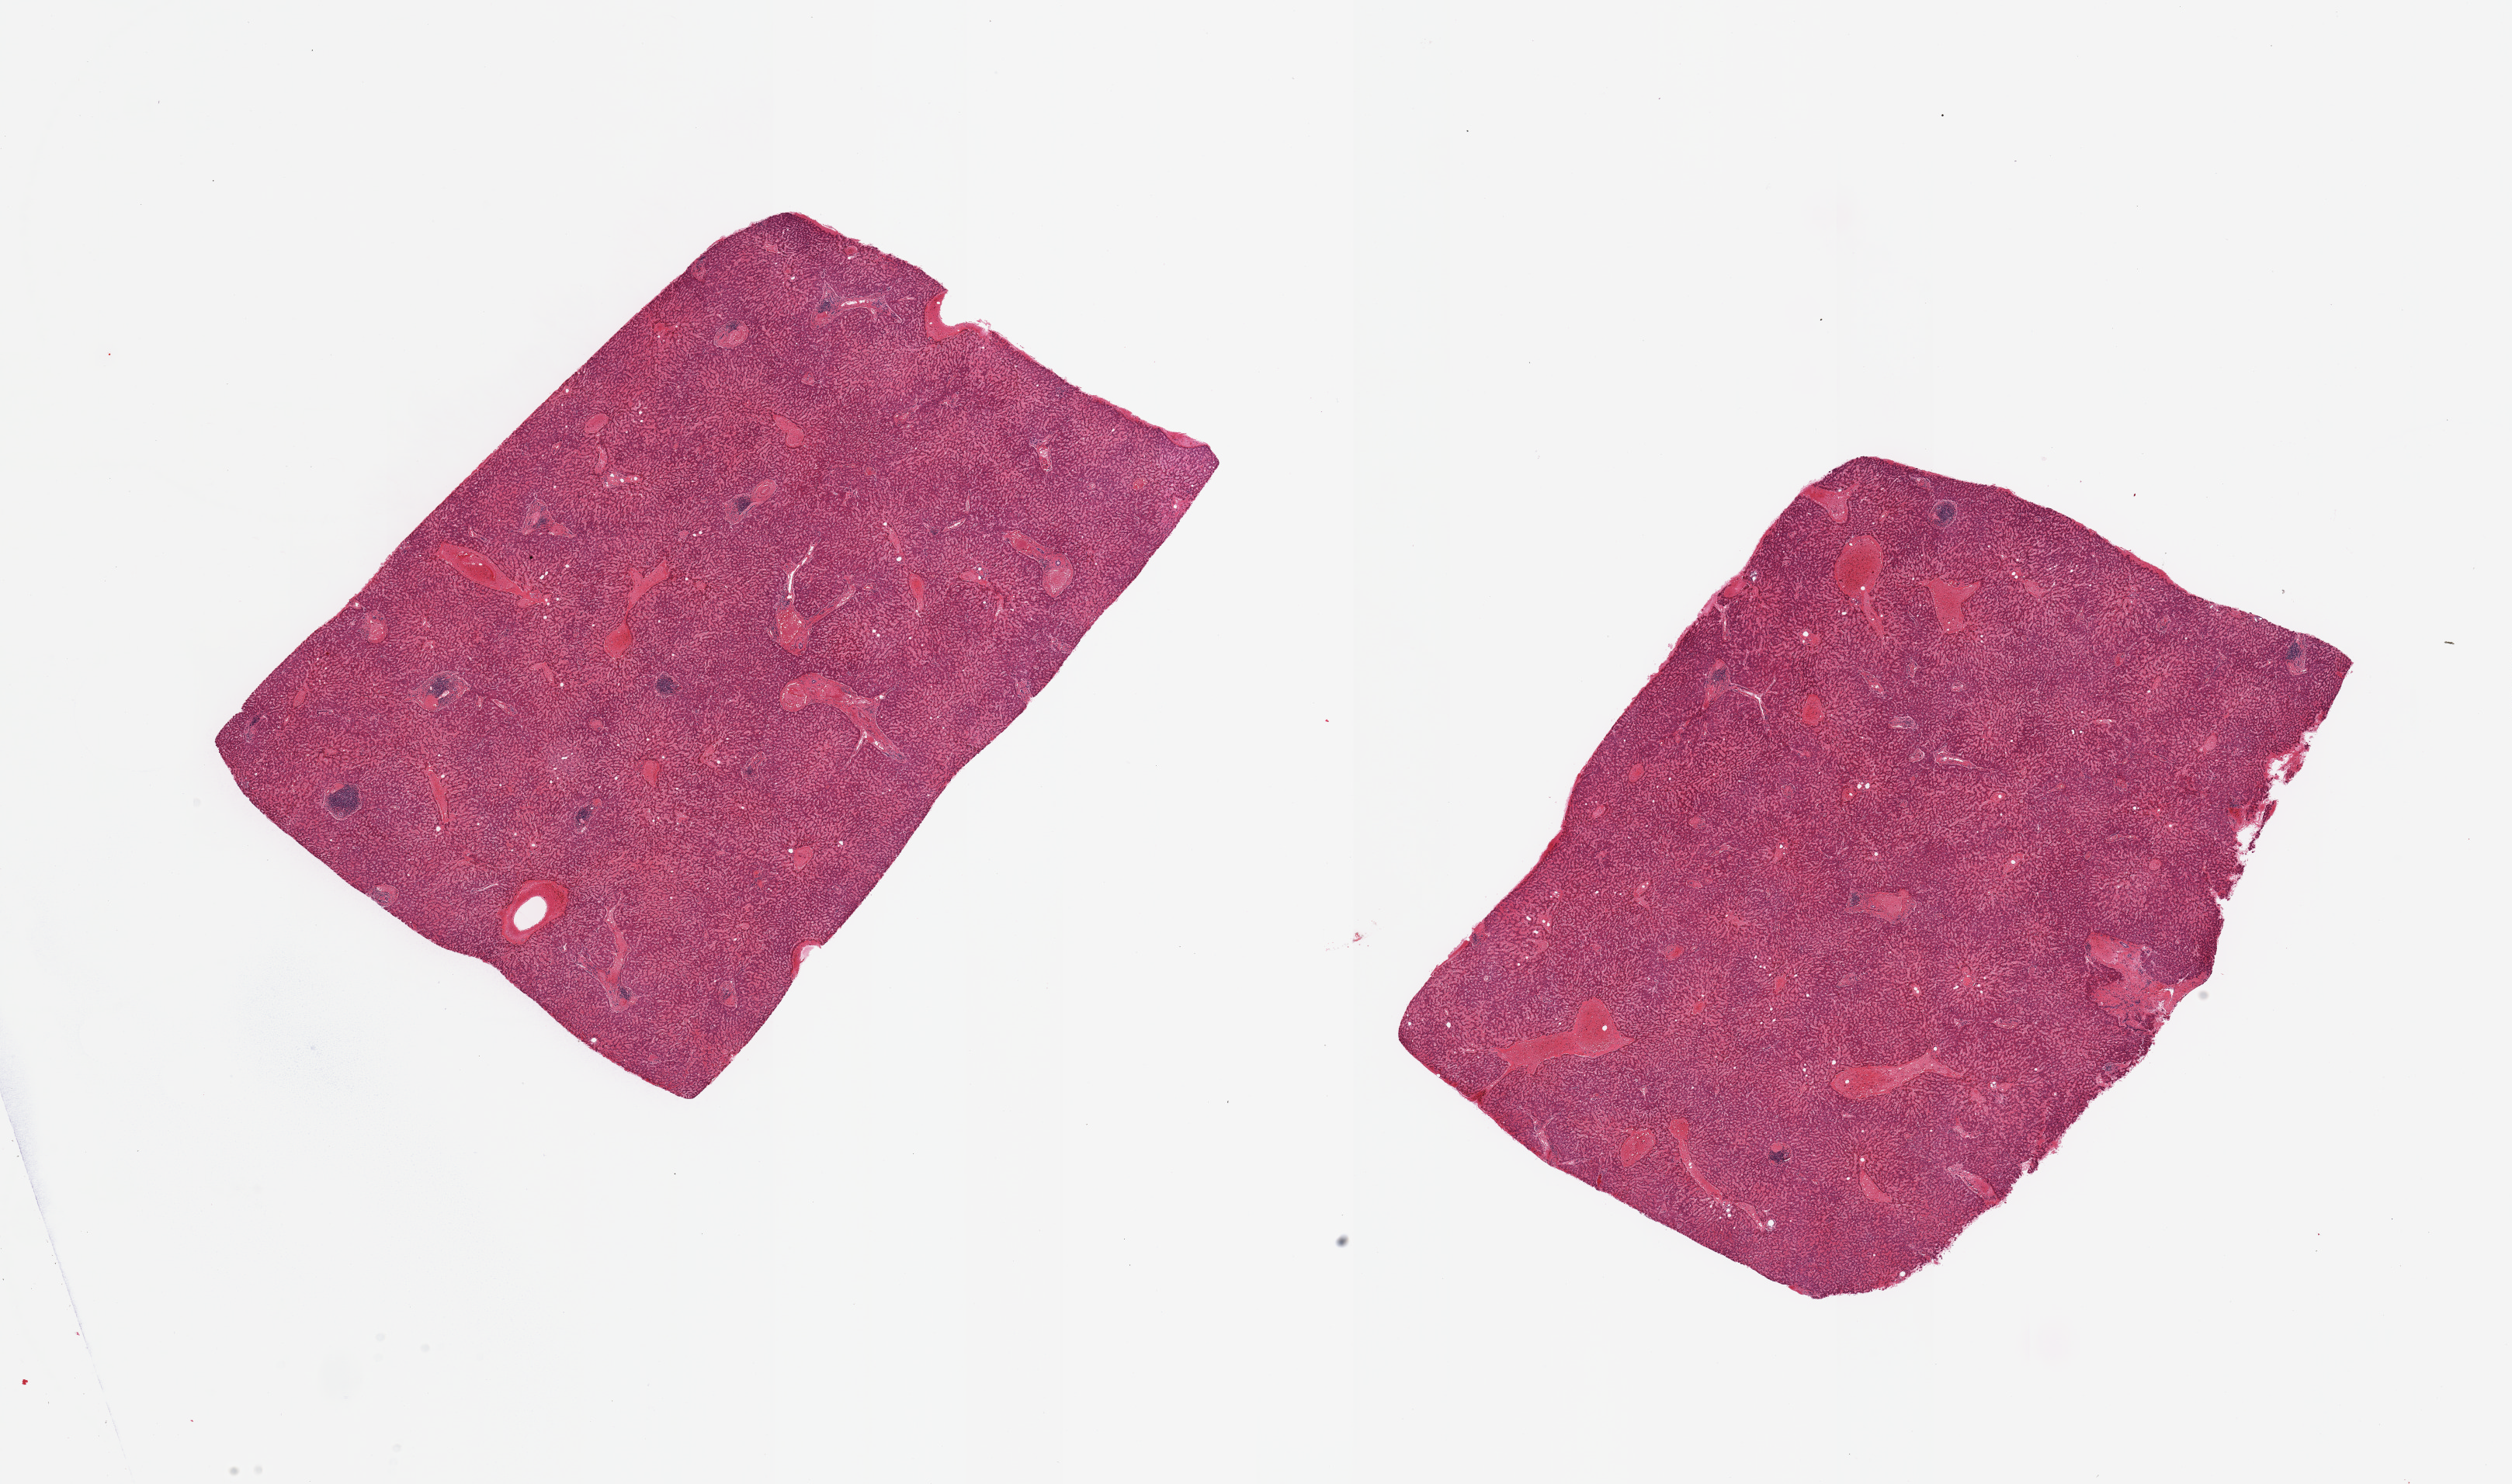
Digitized H&E-stained section, a low-resolution overview of the entire scanned area, about 25.6 x 15.1 mm (from a 20x scan); PAXgene-fixed paraffin-embedded (PFPE) section; target tissue: liver; tissue donor sample.
Review note (as recorded): 2 pieces, moderate passive congestion.